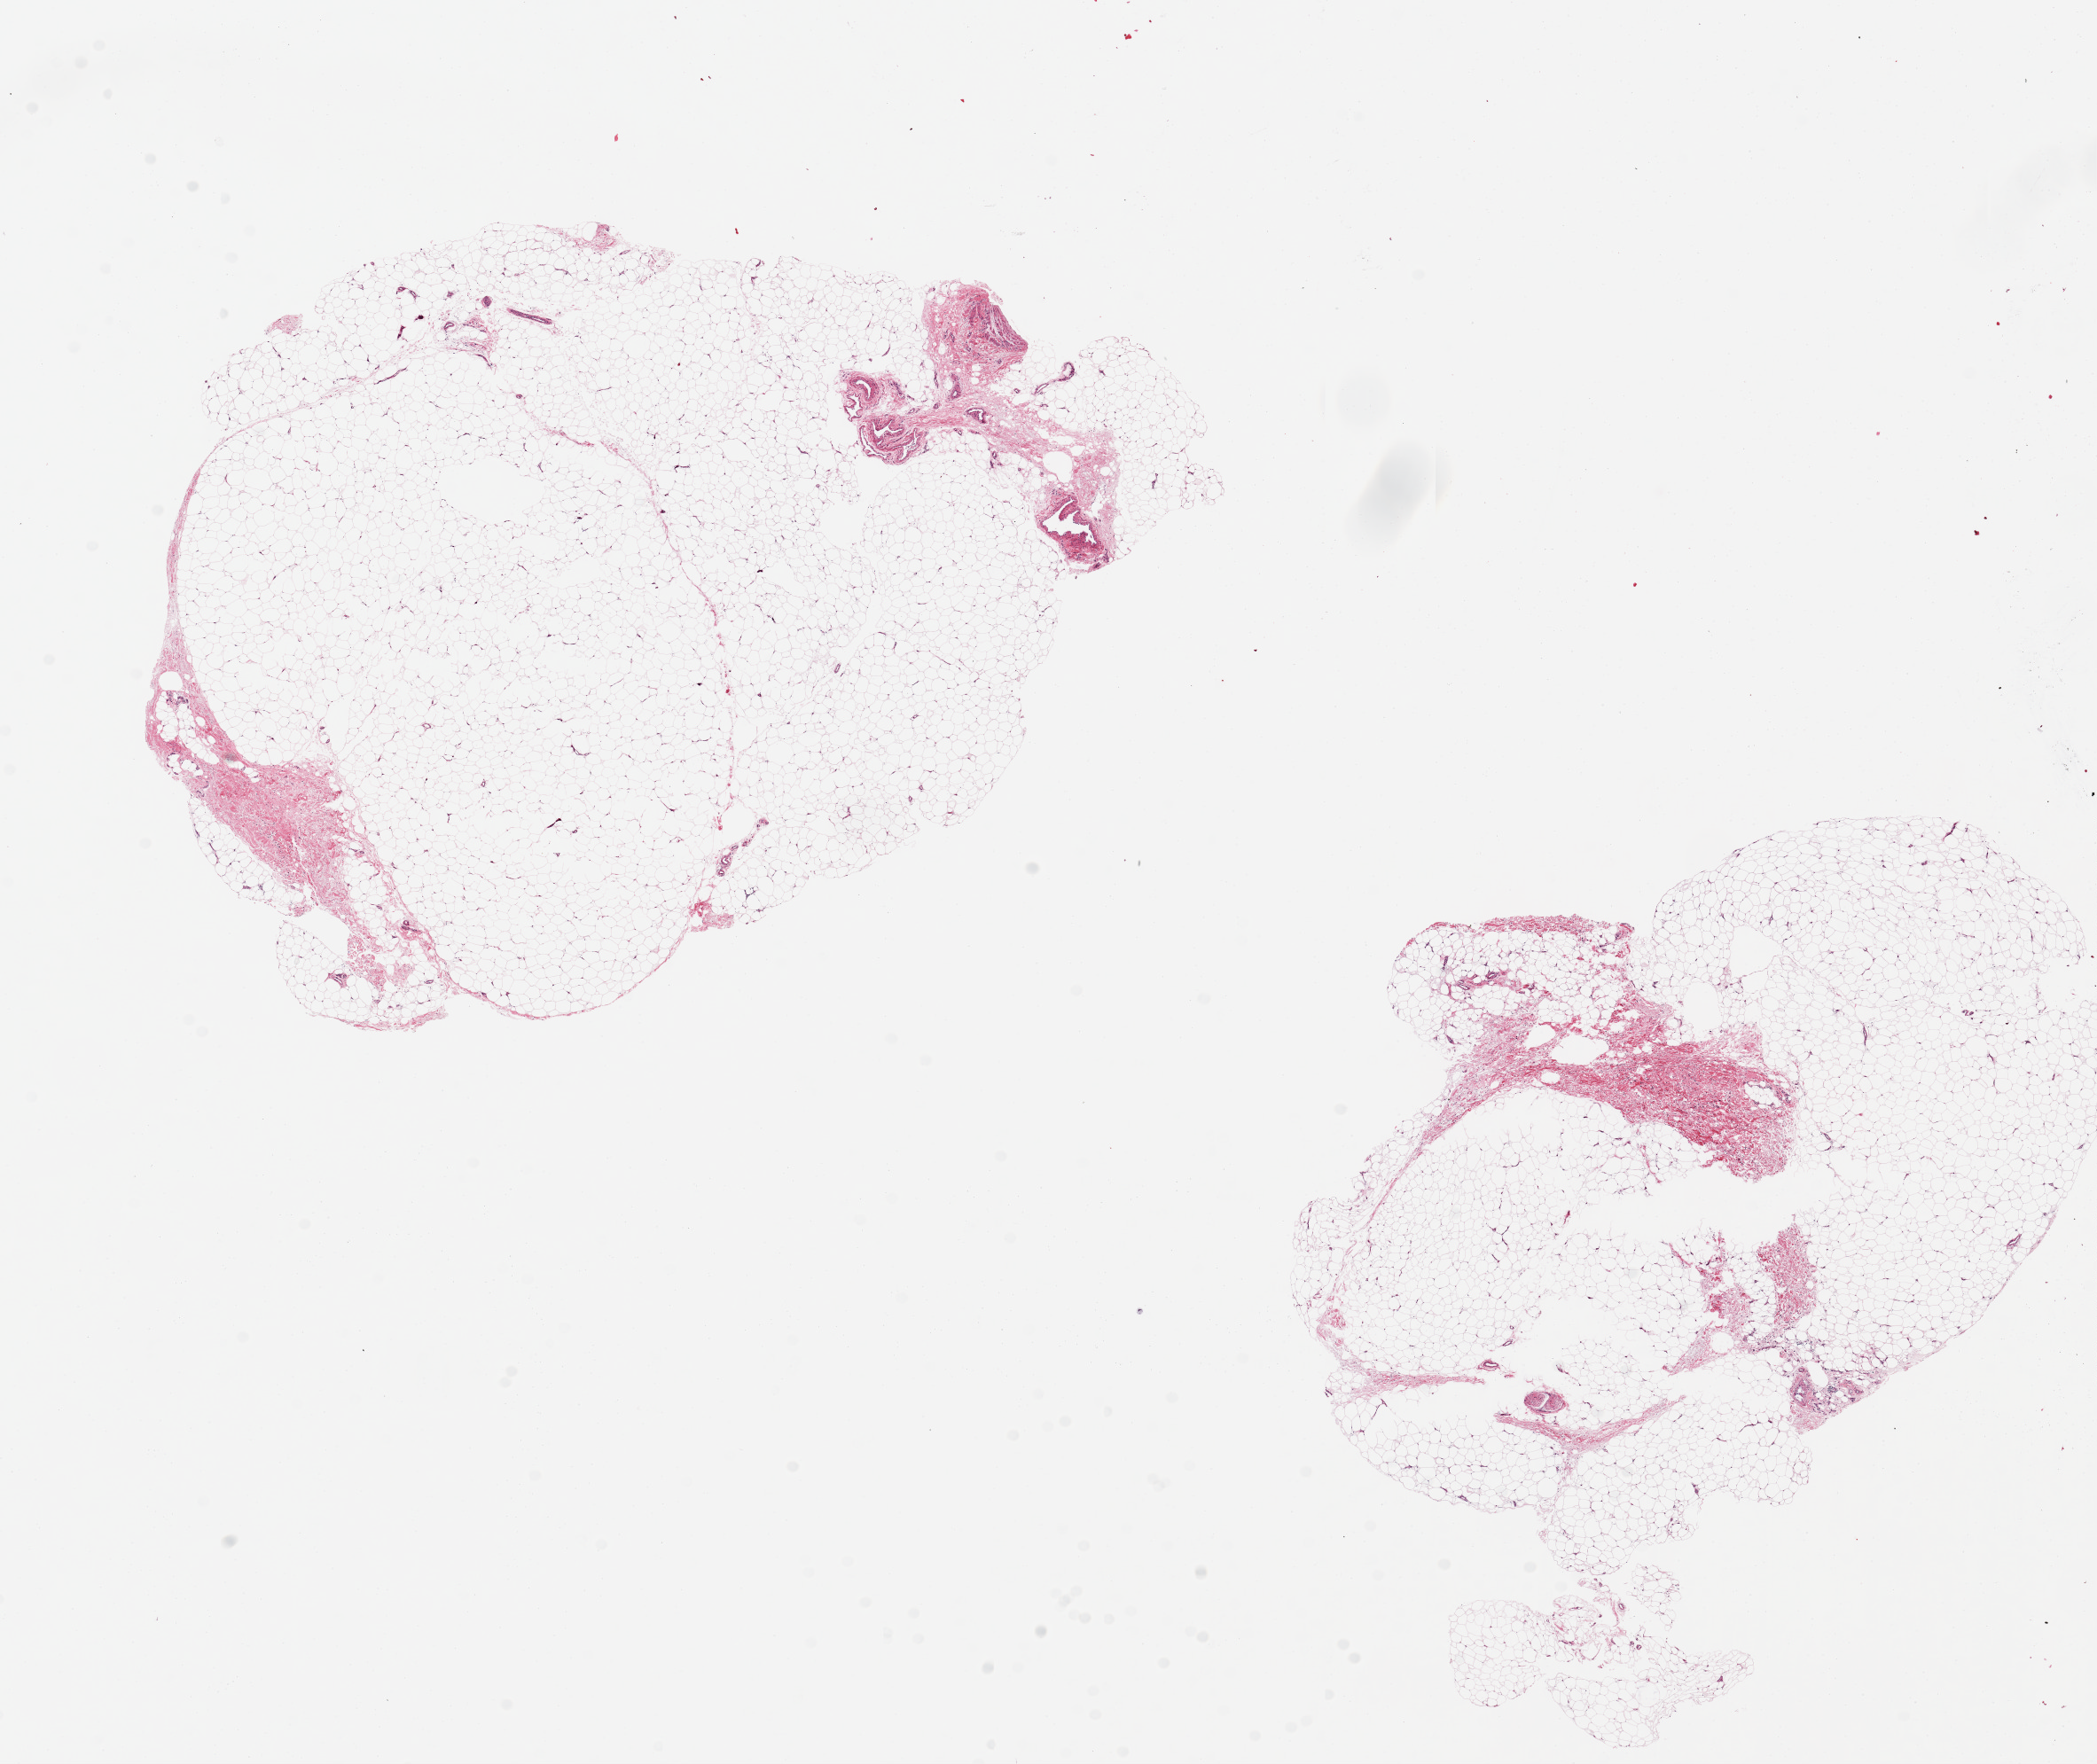
Digitized H&E-stained section, low-resolution overview of the scanned area, about 18.7 x 15.7 mm (acquisition: 20x scan); PAXgene-fixed paraffin-embedded (PFPE) section; sampled site (target tissue): adipose tissue; tissue donor sample. Donor sex: female.
Reviewer comment on this tissue sample: 2 pieces ~8x6mm.